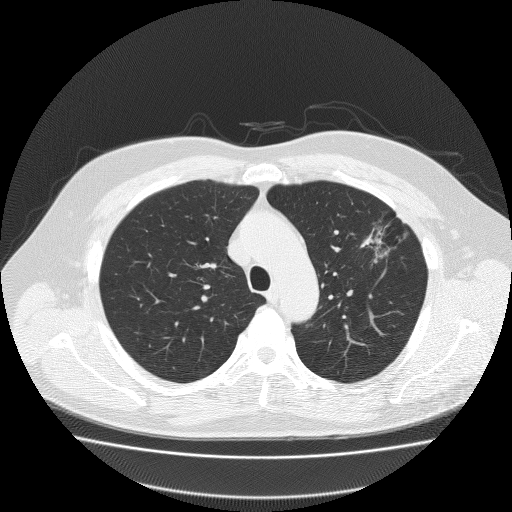
Low-dose screening chest CT, axial slice; baseline annual screen; lung window (W 1500 / L -600 HU); 2 mm slice thickness; lung (sharp) reconstruction kernel (FC51); slice 55 of 204 in the series; 512 × 512 image matrix. Male, age 62 years at enrolment.
- Expert-annotated lung lesion, bounding box [x1, y1, x2, y2] px = [354, 204, 422, 262].
- Reader record for this screening exam (exam-level; its link to the box is not recorded): non-calcified nodule or mass ≥4 mm, left upper lobe, 18 × 8 mm, spiculated (stellate) margins, soft tissue attenuation.
- Official screen result: positive, change unspecified: nodule(s) >= 4 mm or enlarging nodule(s), mass(es), or other non-specific abnormalities suspicious for lung cancer.
- Later outcome: lung cancer diagnosed 49 days after this screen — bronchiolo-alveolar adenocarcinoma, NOS, left upper lobe, well differentiated (G1), stage IA (AJCC 6th edition), 25 mm at pathology.